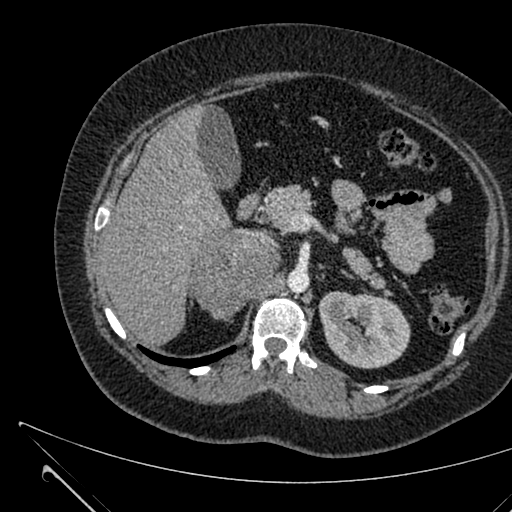
Contrast-enhanced abdominal CT, one axial slice; position 411 of 731 along the scan axis; 120 kVp; intravenous contrast given; soft-tissue window (W 400 / L 40 HU); 1 mm slice thickness; 512 × 512 image matrix, field of view 376 × 376 mm. Female patient, age 36 years. Case-level facts recorded for this patient, not image findings: diagnosis: adrenocortical carcinoma; tumour side: right adrenal; tumour size at pathology: 10 cm; Ki-67 index: 20 %; stage (as recorded): 4.
Annotated regions visible in this slice (semi-automatic segmentation, software-assisted and operator-edited):
- mass: bounding box [x1, y1, x2, y2] px = [195, 230, 275, 318]